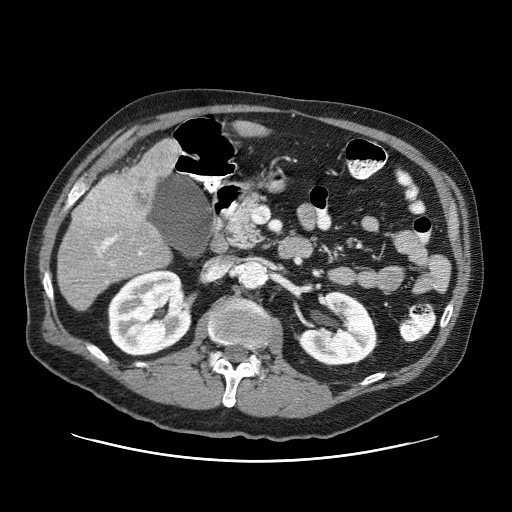
Contrast-enhanced abdominal CT (liver protocol), one axial slice. Position 26 of 87 along the scan axis. Reconstruction kernel STANDARD. One of 3 acquisitions stored at this slice position. Soft-tissue window (W 400 / L 40 HU). 2.5 mm slice thickness. 512 × 512 image matrix. Case-level facts recorded for this patient, not image findings: diagnosis: hepatocellular carcinoma (patient treated with transarterial chemoembolisation; whether this scan precedes or follows treatment is not stated here); TNM stage (as recorded): Stage-IIIA; Child-Pugh class: A.
Annotated regions visible in this slice (semi-automatically segmented with operator editing):
- liver parenchyma outside the tumour (the mass and vessels are separate outlines, so this box may not span the whole liver): bounding box (x1, y1, x2, y2) in pixels: (58, 138, 180, 310)
- mass: (74, 162, 156, 228)
- liver vessels: (95, 235, 142, 266)